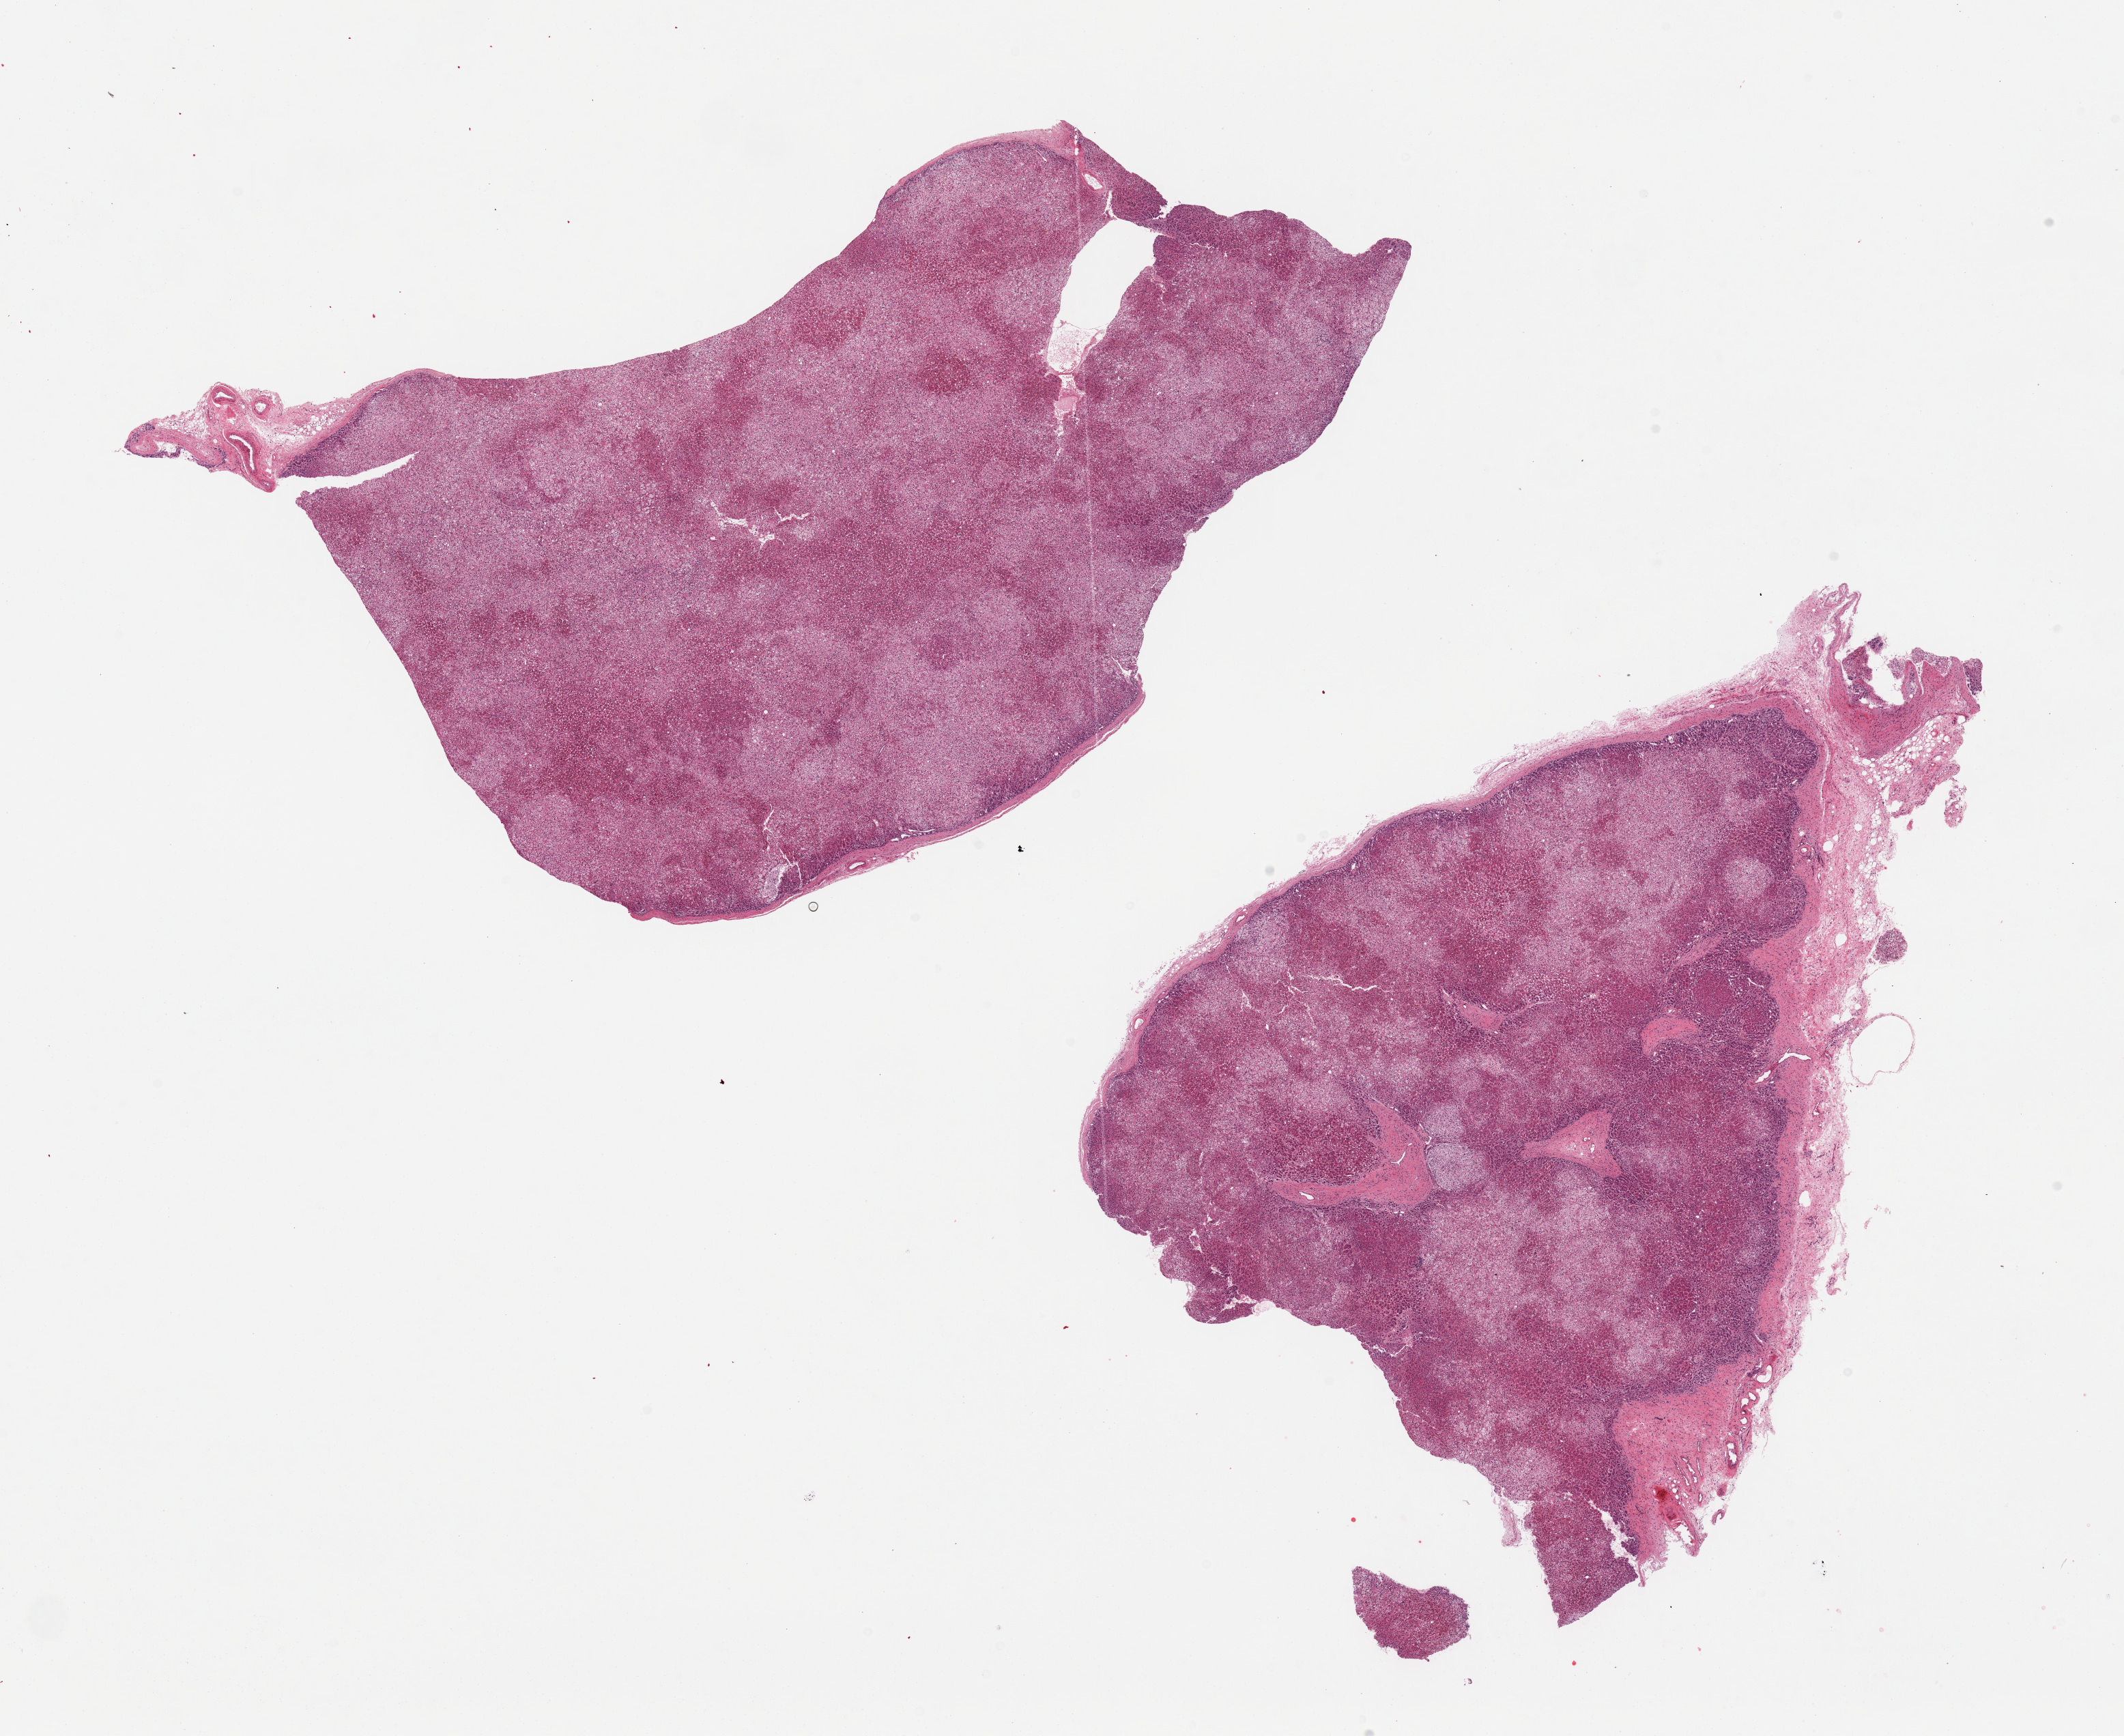
Haematoxylin and eosin whole-slide image — low-resolution overview of the scanned area, about 24.6 x 20.1 mm; PAXgene-fixed paraffin-embedded (PFPE) section; target tissue: adrenal gland; donor tissue sample. Female donor.
Reviewer comment on this tissue sample: 2 pieces, all cortex, well preserved.